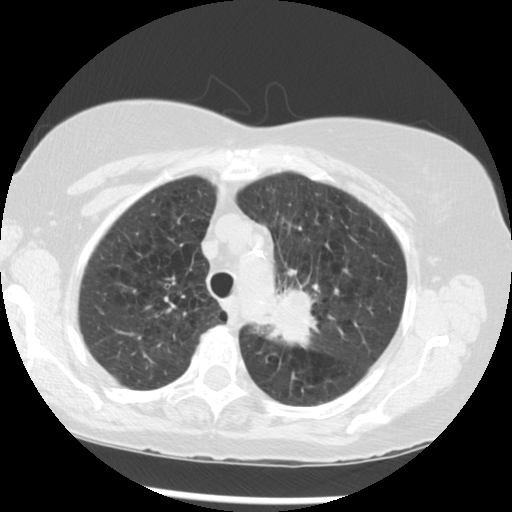
Low-dose screening chest CT, one axial slice. Position 220 of 283 along the scan axis. Reconstruction kernel STANDARD. Lung window (W 1500 / L -600 HU). 2.5 mm slice thickness. 512 × 512 image matrix, field of view 330 × 330 mm.
Structures marked on this image (outlined manually by an expert reader):
- lesion 1 (tumor, upper lobe of left lung): bounding box <262,290,316,345> (left, top, right, bottom; pixels)